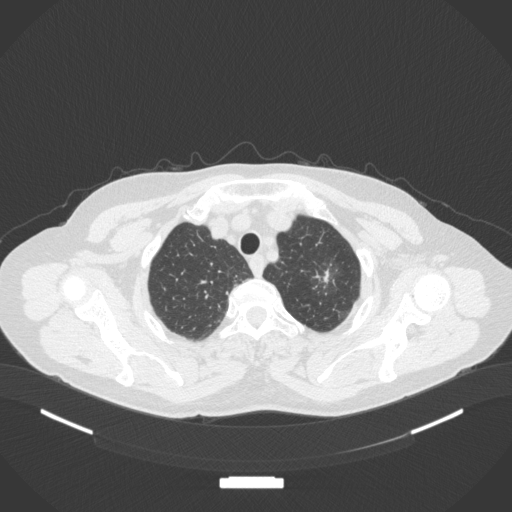
Chest CT, one axial slice. Position 313 of 369 along the scan axis. 120 kVp. Lung window (W 1500 / L -600 HU). 1 mm slice thickness. 512 × 512 image matrix, field of view 400 × 400 mm. Patient: female, 64 years. From the clinical record (not read from this slice): clinical TNM (as recorded): T1c N0 M0; histopathological grade: G1.
Structures marked on this image (rectangle marked by the reading radiologist):
- lung tumour (recorded histology: adenocarcinoma): bounding box [x1, y1, x2, y2] px = [304, 252, 353, 303]